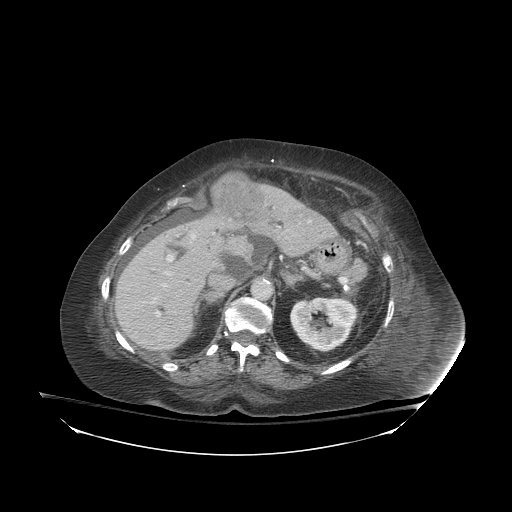
Contrast-enhanced abdominal CT (liver protocol), one axial slice; position 53 of 81 along the scan axis; 140 kVp; soft-tissue window (W 400 / L 40 HU); 2.5 mm slice thickness; 512 × 512 image matrix. From the clinical record (not read from this slice): diagnosis: hepatocellular carcinoma (patient treated with transarterial chemoembolisation; whether this scan precedes or follows treatment is not stated here); TNM stage (as recorded): Stage-I; Child-Pugh class: B.
Outlined on this slice (semi-automatic segmentation, software-assisted and operator-edited):
- liver parenchyma outside the tumour (the mass and vessels are separate outlines, so this box may not span the whole liver): bounding box (x1, y1, x2, y2) in pixels: (114, 184, 336, 350)
- mass: (213, 172, 264, 221)
- liver vessels: (151, 233, 214, 317)